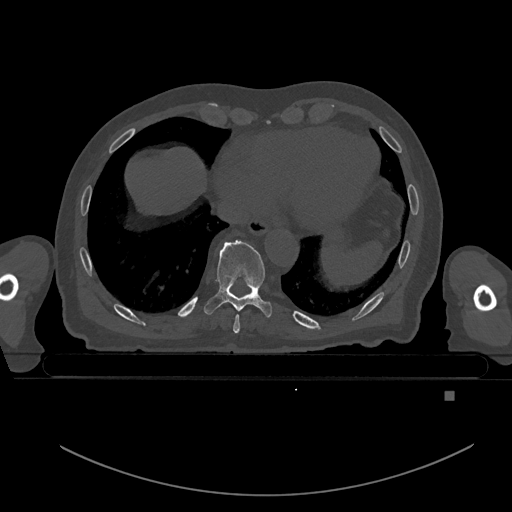
CT including the spine, one axial slice. Slice 150 of 969 in the series (ordered by position). Bone window (W 1800 / L 400 HU). 0.5 mm slice thickness. 512 × 512 image matrix. Patient: male, 82 years. Case-level facts recorded for this patient, not image findings: primary cancer: prostate; vertebrae with lytic lesions (as recorded): T11, T9, T8, T2.
Structures marked on this image (semi-automatically segmented with operator editing):
- T8 vertebra: bounding box <233,314,240,333> (left, top, right, bottom; pixels)
- T9 vertebra: <204,240,272,318>